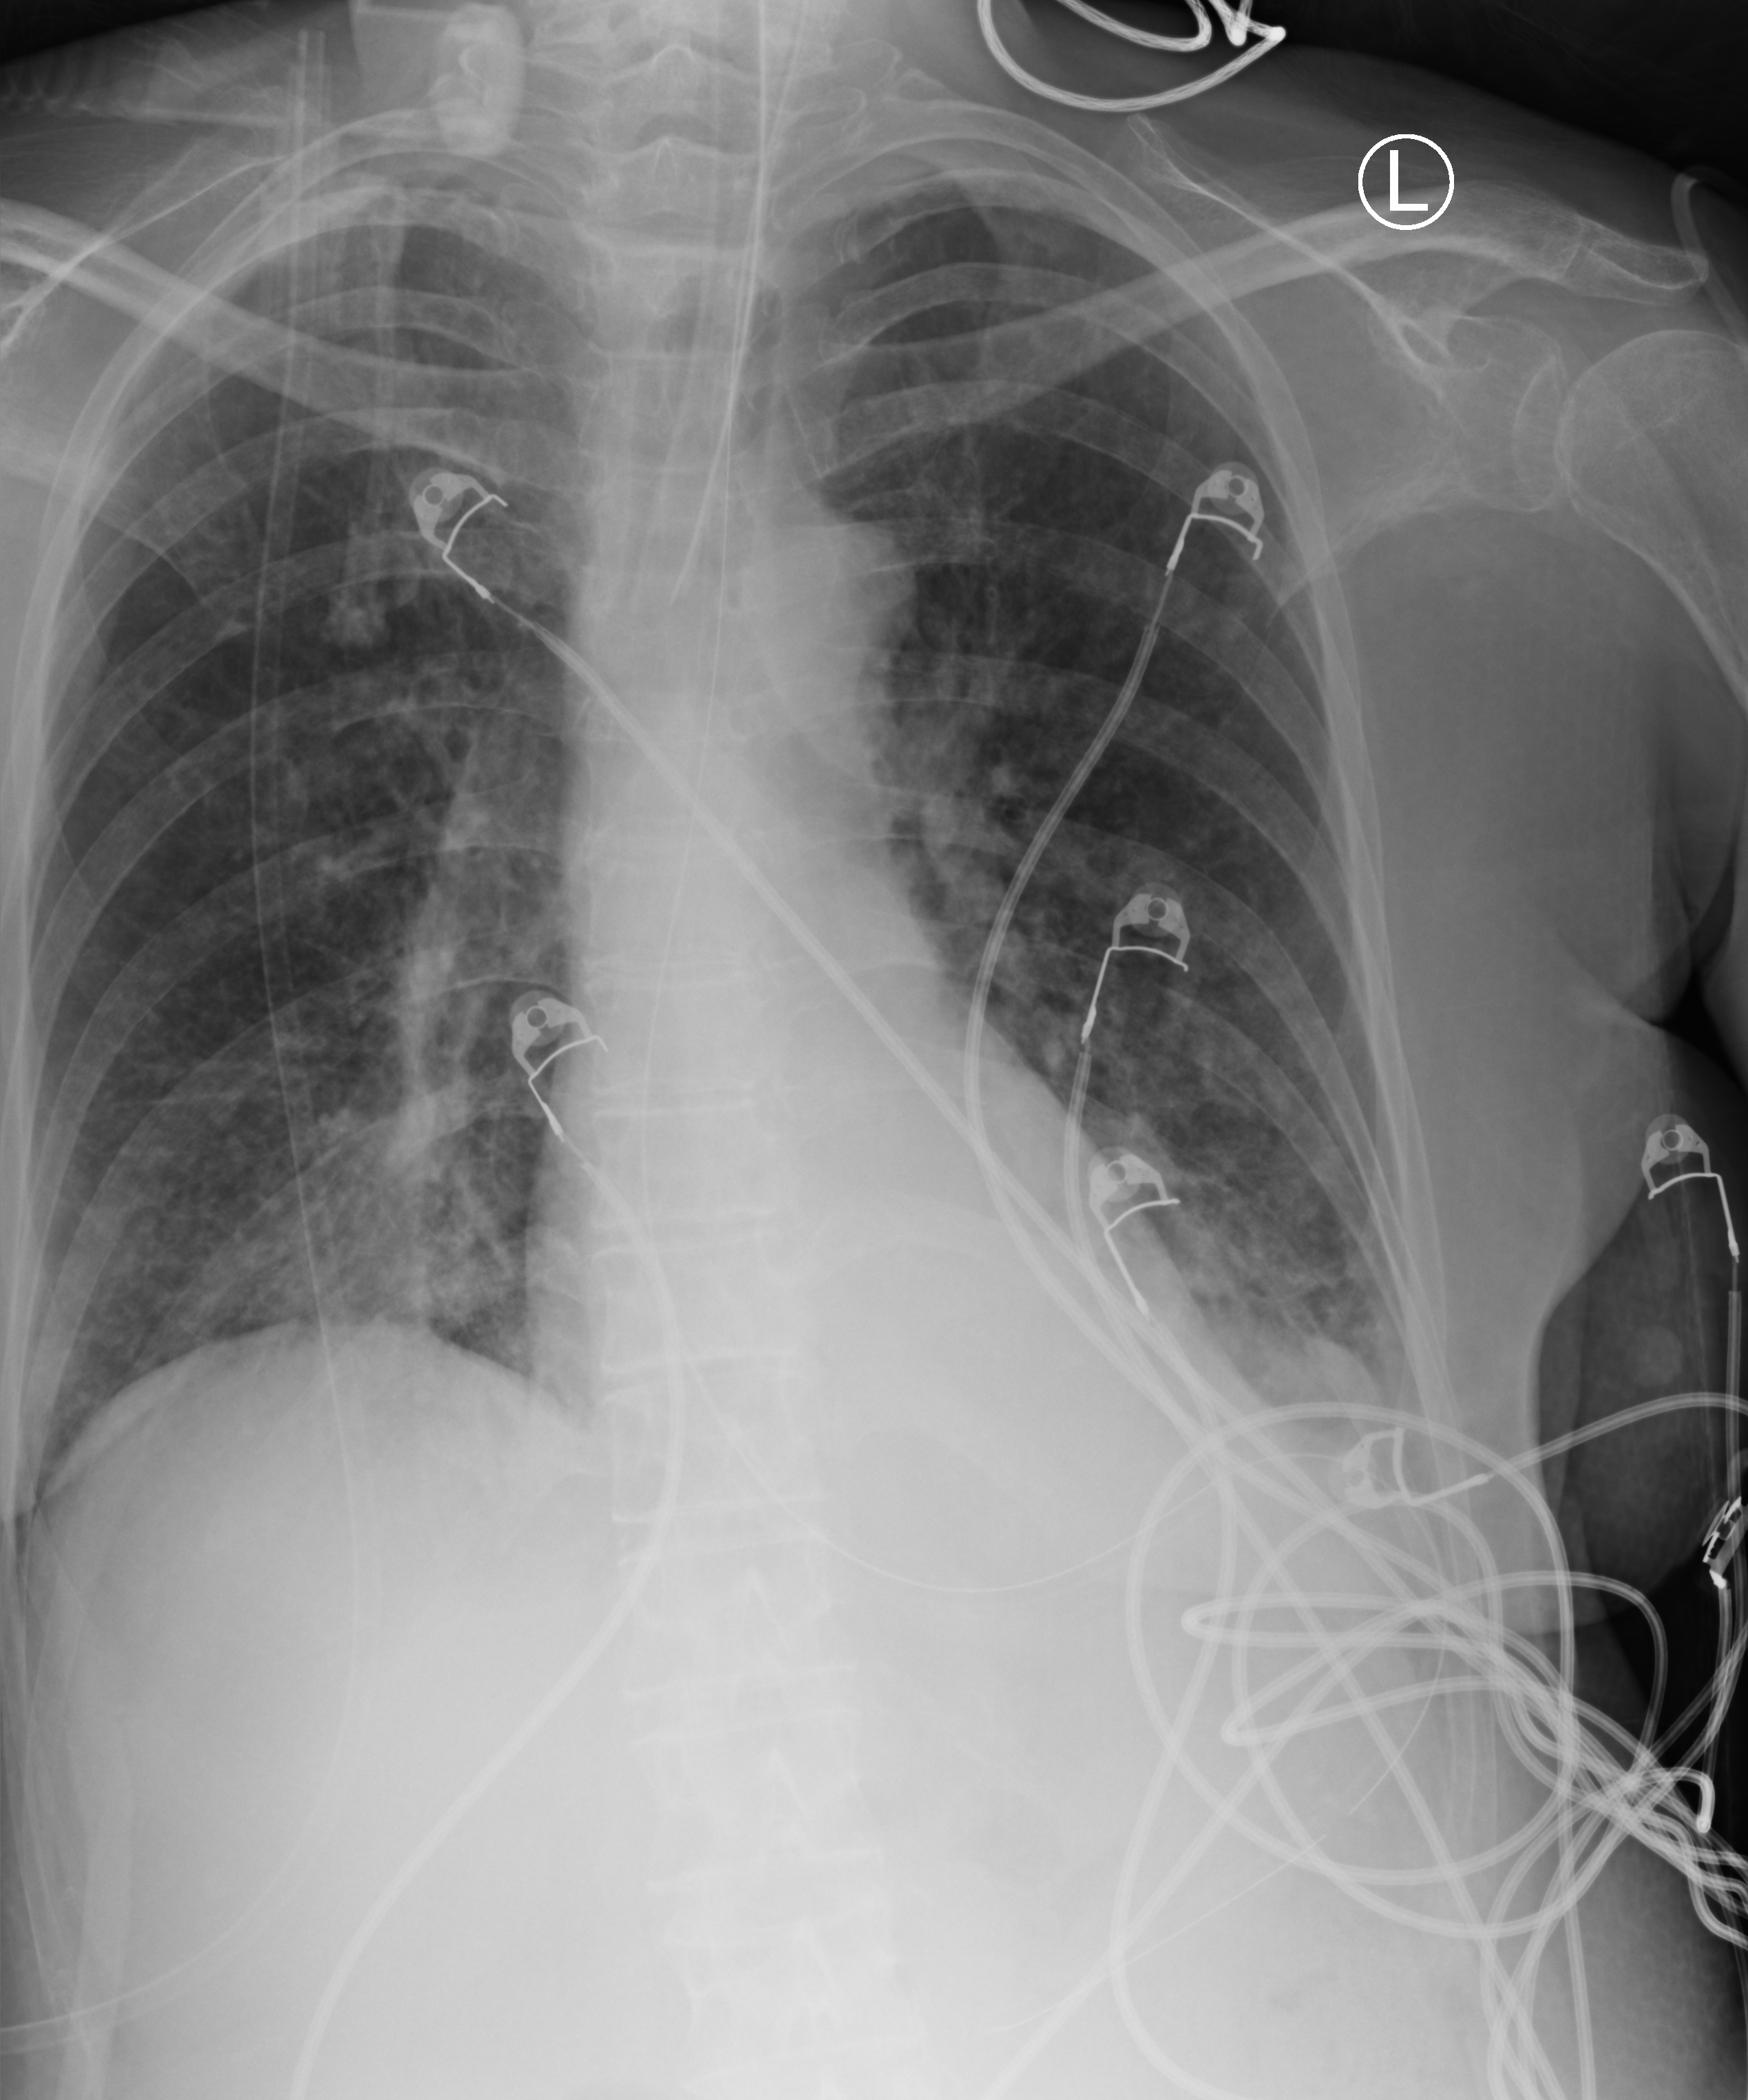
Bedside chest radiograph (computed radiography); anteroposterior (AP) projection. Adult patient hospitalised with COVID-19, age 18–59 years.
Admission-level facts for this patient (not findings on this image; timing relative to this image not recorded):
- admitted to intensive care during this hospital stay: yes
- mechanically ventilated during this hospital stay: yes